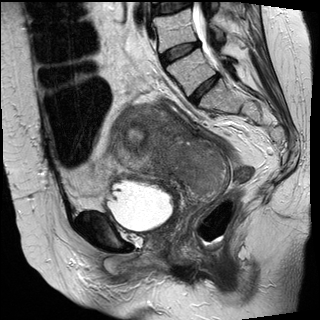
Pelvic MRI for cervical cancer, one sagittal slice. Slice 16 of 30 in the series (ordered by position). T2-weighted. 1.5 T. TE 89 ms, TR 3810 ms. 4 mm slice thickness. 320 × 320 image matrix, field of view 260 × 260 mm. Patient: female, 62 years.
Outlined on this slice (manually delineated by an expert):
- uterus and cervix: box from (x=110, y=103) to (x=231, y=202) px